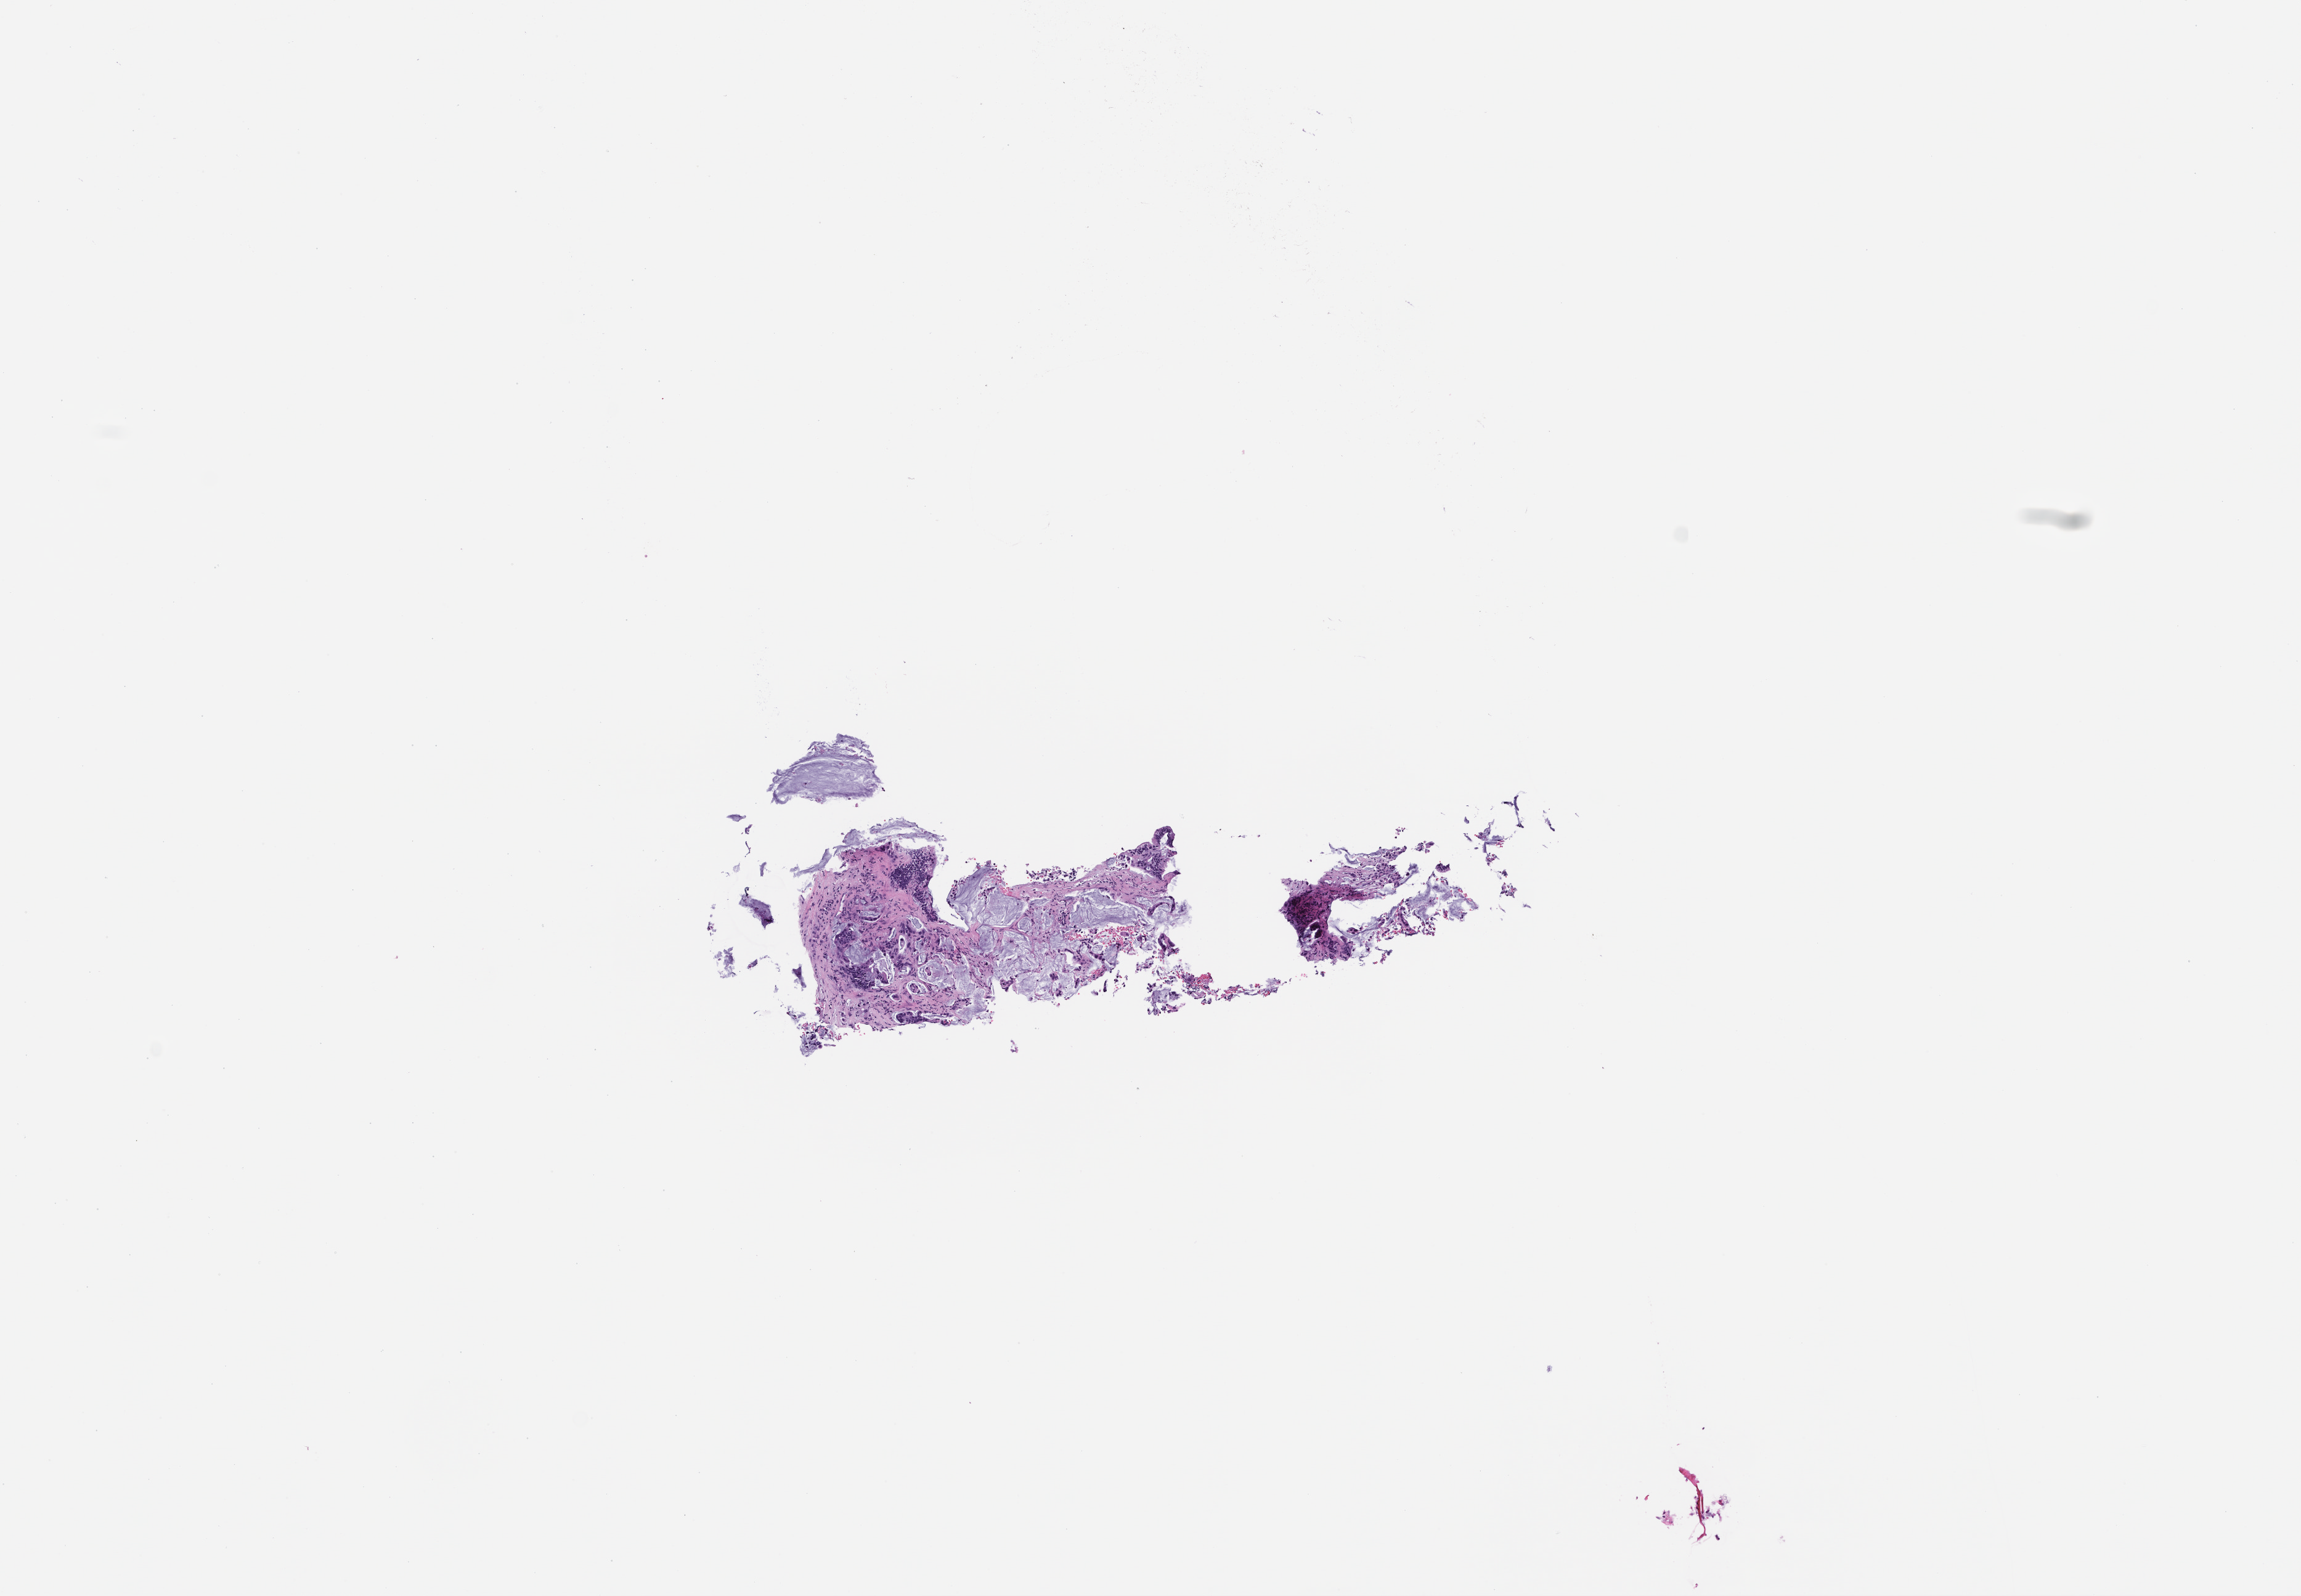
Whole-slide image, haematoxylin and eosin stain — whole scanned area (about 7.5 x 5.2 mm) shown as a low-resolution overview, formalin-fixed paraffin-embedded section, archival tissue. Patient: male.
This section: metastasis (sampled organ not recorded). Patient diagnosis (primary): Colorectal Carcinoma.